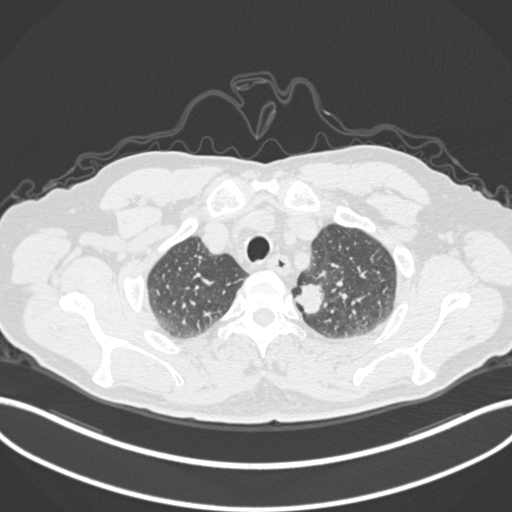
Chest CT, one axial slice. Position 274 of 306 along the scan axis. Reconstruction kernel B30f. 120 kVp. Lung window (W 1500 / L -600 HU). 512 × 512 image matrix. Male patient, age 64 years. From the clinical record (not read from this slice): clinical TNM (as recorded): T1c N0 M0.
Structures marked on this image (rectangle marked by the reading radiologist):
- lung tumour (recorded histology: adenocarcinoma): bounding box <293,279,329,322> (left, top, right, bottom; pixels)